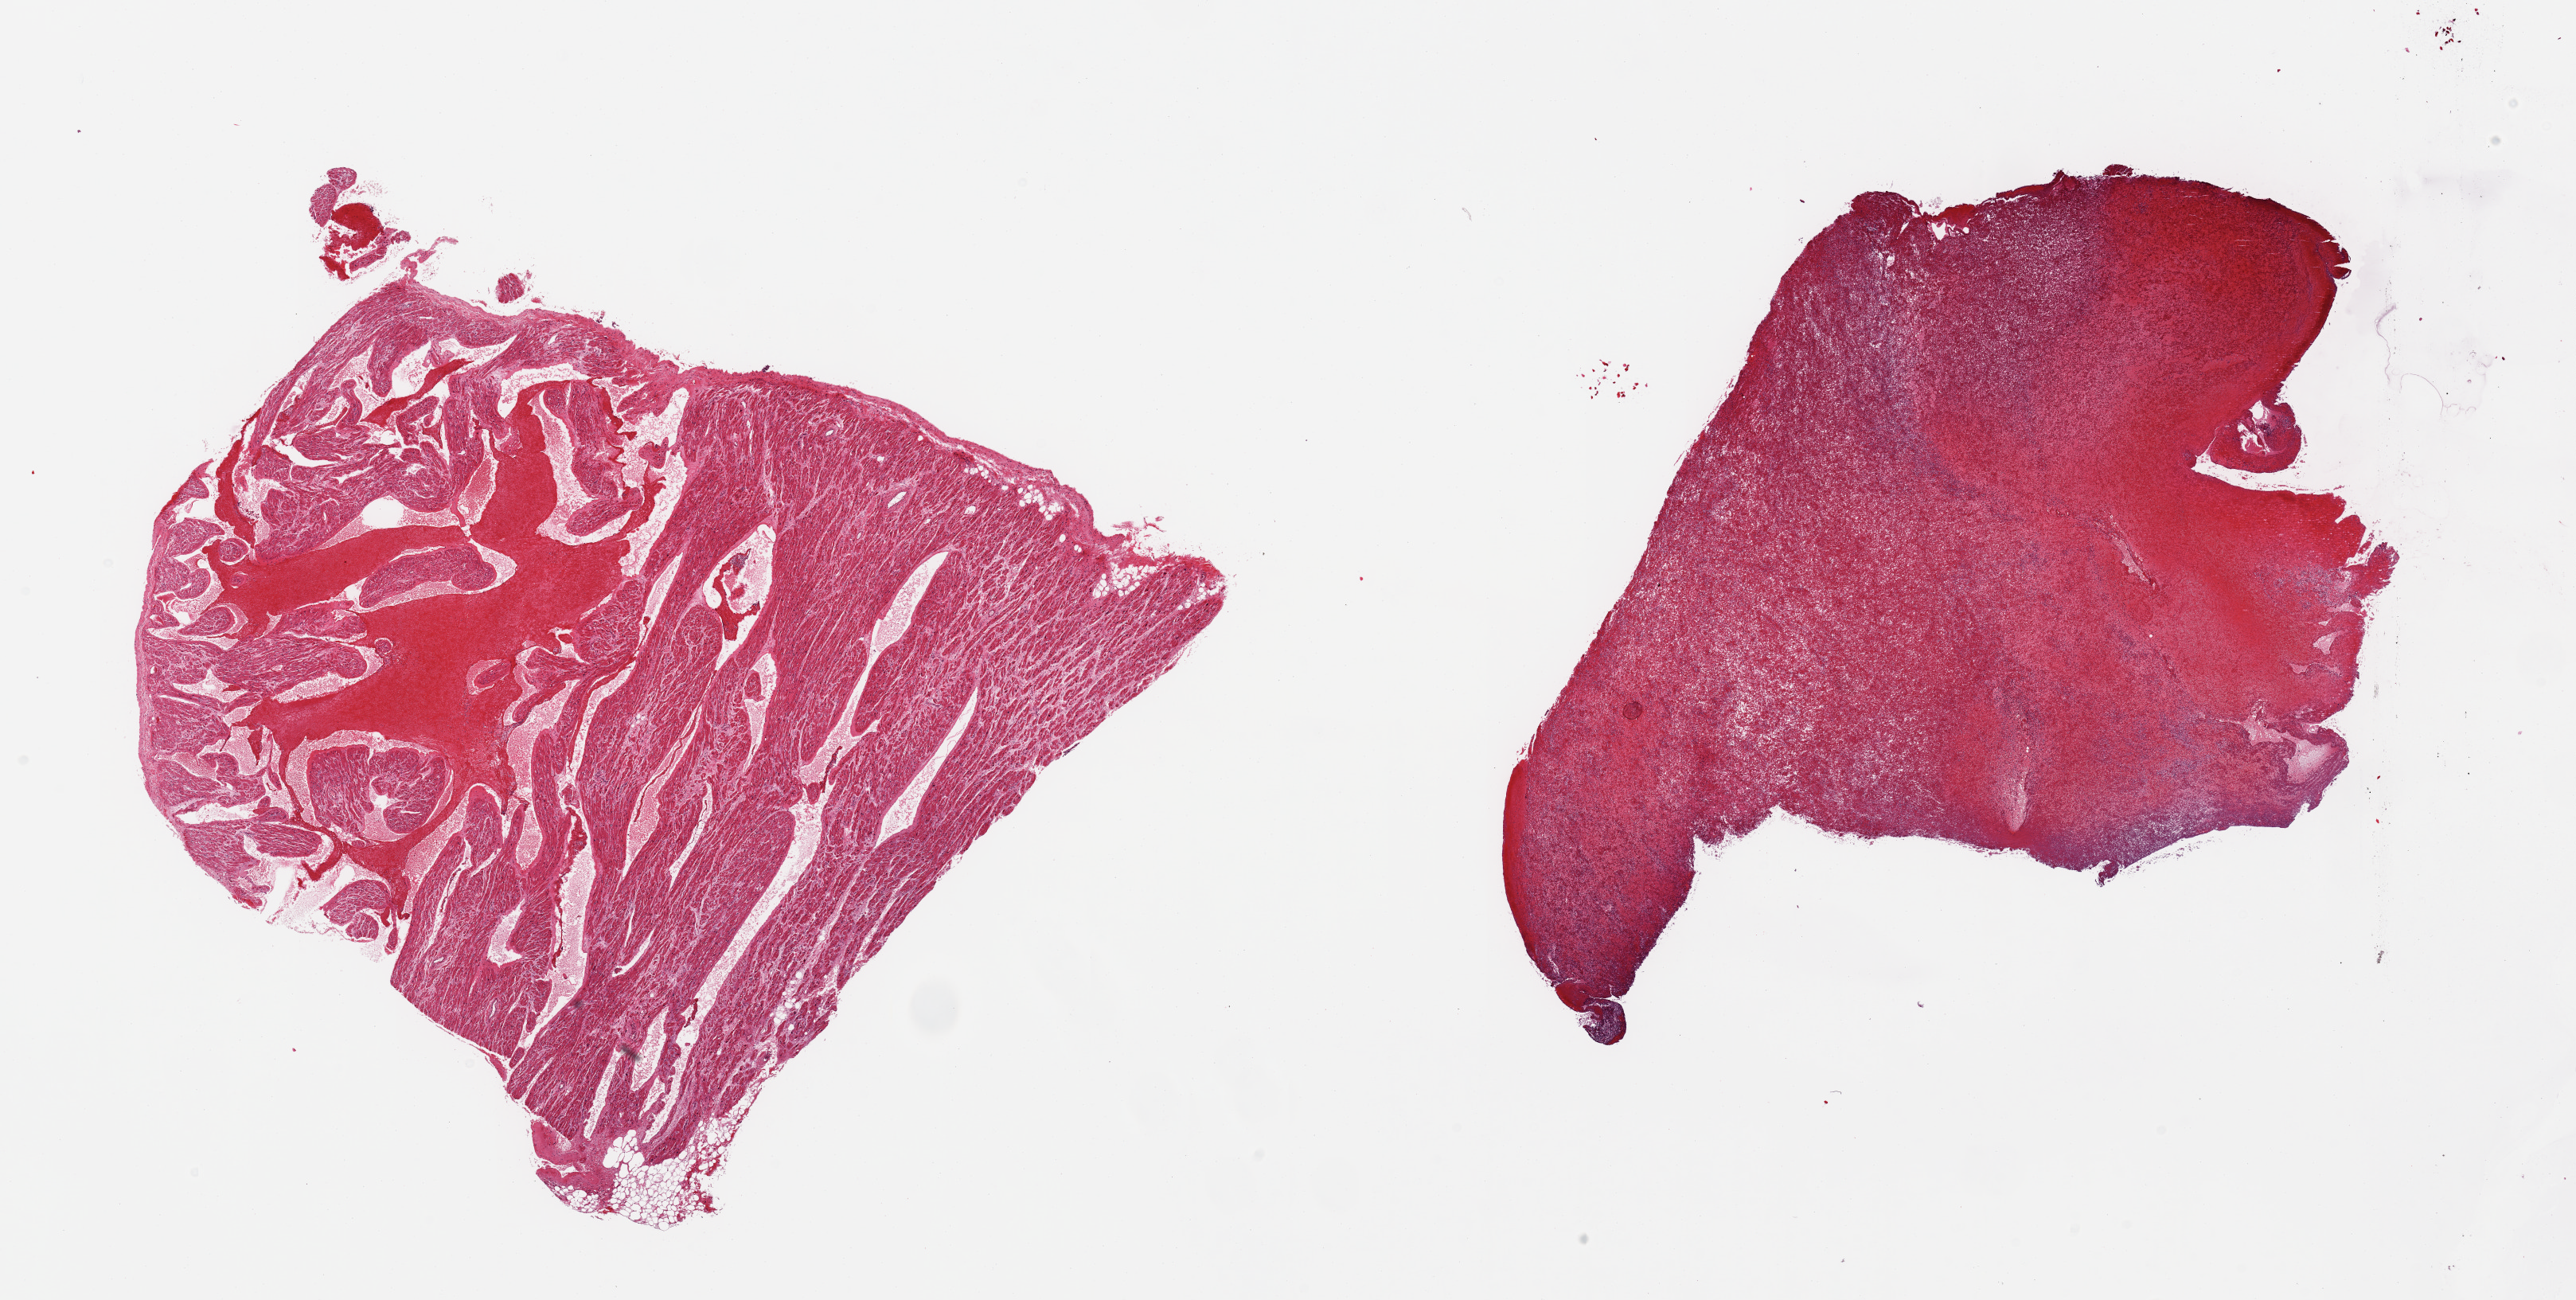
Whole-slide image, haematoxylin and eosin stain — a low-resolution overview of the entire scanned area, about 25.6 x 12.9 mm. PAXgene-fixed, paraffin-embedded tissue. Section of auricular appendage (target tissue). Donor tissue sample. Male donor.
• reviewer comment on this tissue sample: 2 pieces; 1 contains 20% blood clot; other is all blood clot